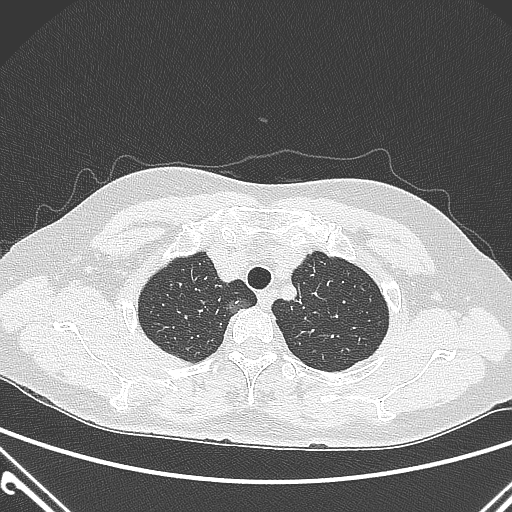
Chest CT, one axial slice. Slice 243 of 300 in the series (ordered by position). Lung window (W 1500 / L -600 HU). 1 mm slice thickness. 512 × 512 image matrix, field of view 350 × 350 mm. Patient: female, 54 years. From the clinical record (not read from this slice): clinical TNM (as recorded): T1a N0 M0.
Annotated regions visible in this slice (rectangle marked by the reading radiologist):
- lung tumour (recorded histology: adenocarcinoma): bounding box <219,289,252,321> (left, top, right, bottom; pixels)